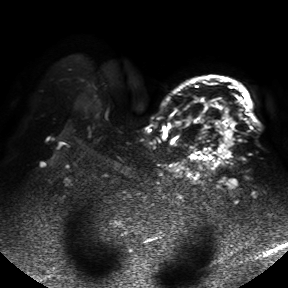
Breast MRI, one axial slice; position 34 of 50 along the scan axis; diffusion-weighted series; image 2 of 4 stored at this slice position (different b-values; order by instance number); 1.5 T; 4 mm slice thickness; 288 × 288 image matrix, field of view 390 × 390 mm. Female patient.
Structures marked on this image (outlined manually by an expert reader):
- tumour on diffusion-weighted imaging: bounding box <218,114,232,159> (left, top, right, bottom; pixels)